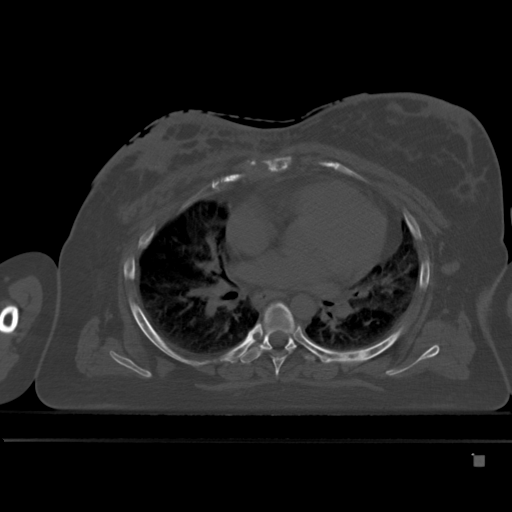
CT including the spine, one axial slice. Slice 312 of 495 in the series (ordered by position). Bone window (W 1800 / L 400 HU). 512 × 512 image matrix. Patient: female, 33 years. From the clinical record (not read from this slice): primary cancer: breast; vertebrae with lytic lesions (as recorded): T1.
Structures marked on this image (semi-automatic segmentation, software-assisted and operator-edited):
- T5 vertebra: bounding box [x1, y1, x2, y2] px = [273, 332, 292, 377]
- T6 vertebra: [240, 308, 318, 364]